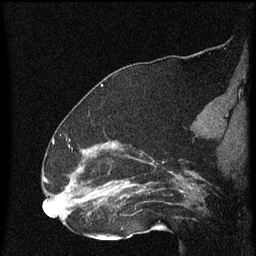
Breast MRI (dynamic contrast-enhanced), one sagittal slice. Slice 34 of 60 in the series (ordered by position). Dynamic contrast-enhanced series, image 2 of 4 at this slice position (ordered by acquisition). 1.5 T. TE 4.2 ms, TR 8 ms. 2 mm slice thickness. 256 × 256 image matrix, field of view 180 × 180 mm. Female patient, age 52 years.
Outlined on this slice (semi-automatic segmentation, software-assisted and operator-edited):
- analysis volume of interest (the breast-tissue region the enhancement analysis was run in; not a lesion): bounding box [x1, y1, x2, y2] px = [73, 148, 172, 219]
- tumour enhancement mask (voxels above the 70 % enhancement threshold inside the analysis volume of interest): [81, 164, 153, 199]